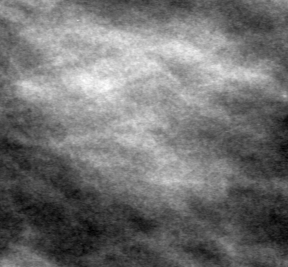
Cropped region of a digitized screen-film mammogram centred on a radiologist-marked abnormality; left breast; MLO view; BI-RADS breast density category 3 (scale 1–4).
- Finding: mass, shape lobulated, margins obscured; BI-RADS assessment category 0 (incomplete: needs additional imaging); subtlety rating 5 on a 1 (subtle) to 5 (obvious) scale; pathology (as recorded): benign.